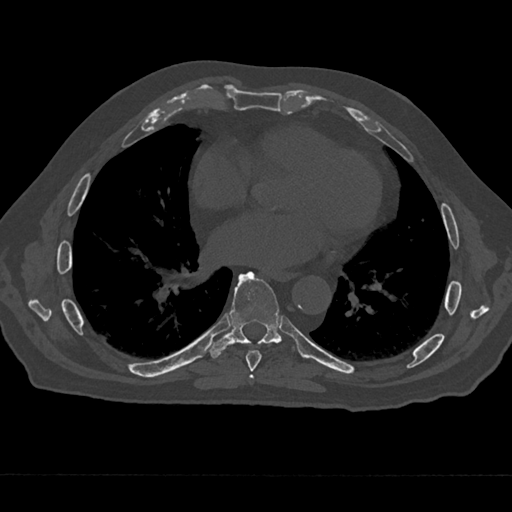
CT including the spine, one axial slice; position 339 of 797 along the scan axis; reconstruction kernel Br40s/3; 120 kVp; bone window (W 1800 / L 400 HU); 0.5 mm slice thickness; 512 × 512 image matrix, field of view 377 × 377 mm. Male patient, age 75 years. From the clinical record (not read from this slice): primary cancer: renal; vertebrae with lytic lesions (as recorded): T4.
Structures marked on this image (semi-automatically segmented with operator editing):
- T6 vertebra: box from (x=249, y=375) to (x=254, y=379) px
- T7 vertebra: (x=242, y=348)–(x=262, y=373)
- T8 vertebra: (x=209, y=271)–(x=282, y=358)